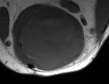
MRI of an extremity soft-tissue mass, one axial slice; position 28 of 50 along the scan axis; MR volume resampled by the dataset authors to the PET/CT grid (not the native acquisition matrix); 3.27 mm slice thickness; 109 × 84 image matrix, field of view 106 × 82 mm. Male patient. Case-level facts recorded for this patient, not image findings: histological type: synovial sarcoma; site of the primary tumour: left poplietal fossa.
Annotated regions visible in this slice (expert contour drawn on MRI and transferred to this co-registered scan by the dataset authors):
- gross tumour volume (mass): bounding box [x1, y1, x2, y2] px = [14, 14, 85, 70]